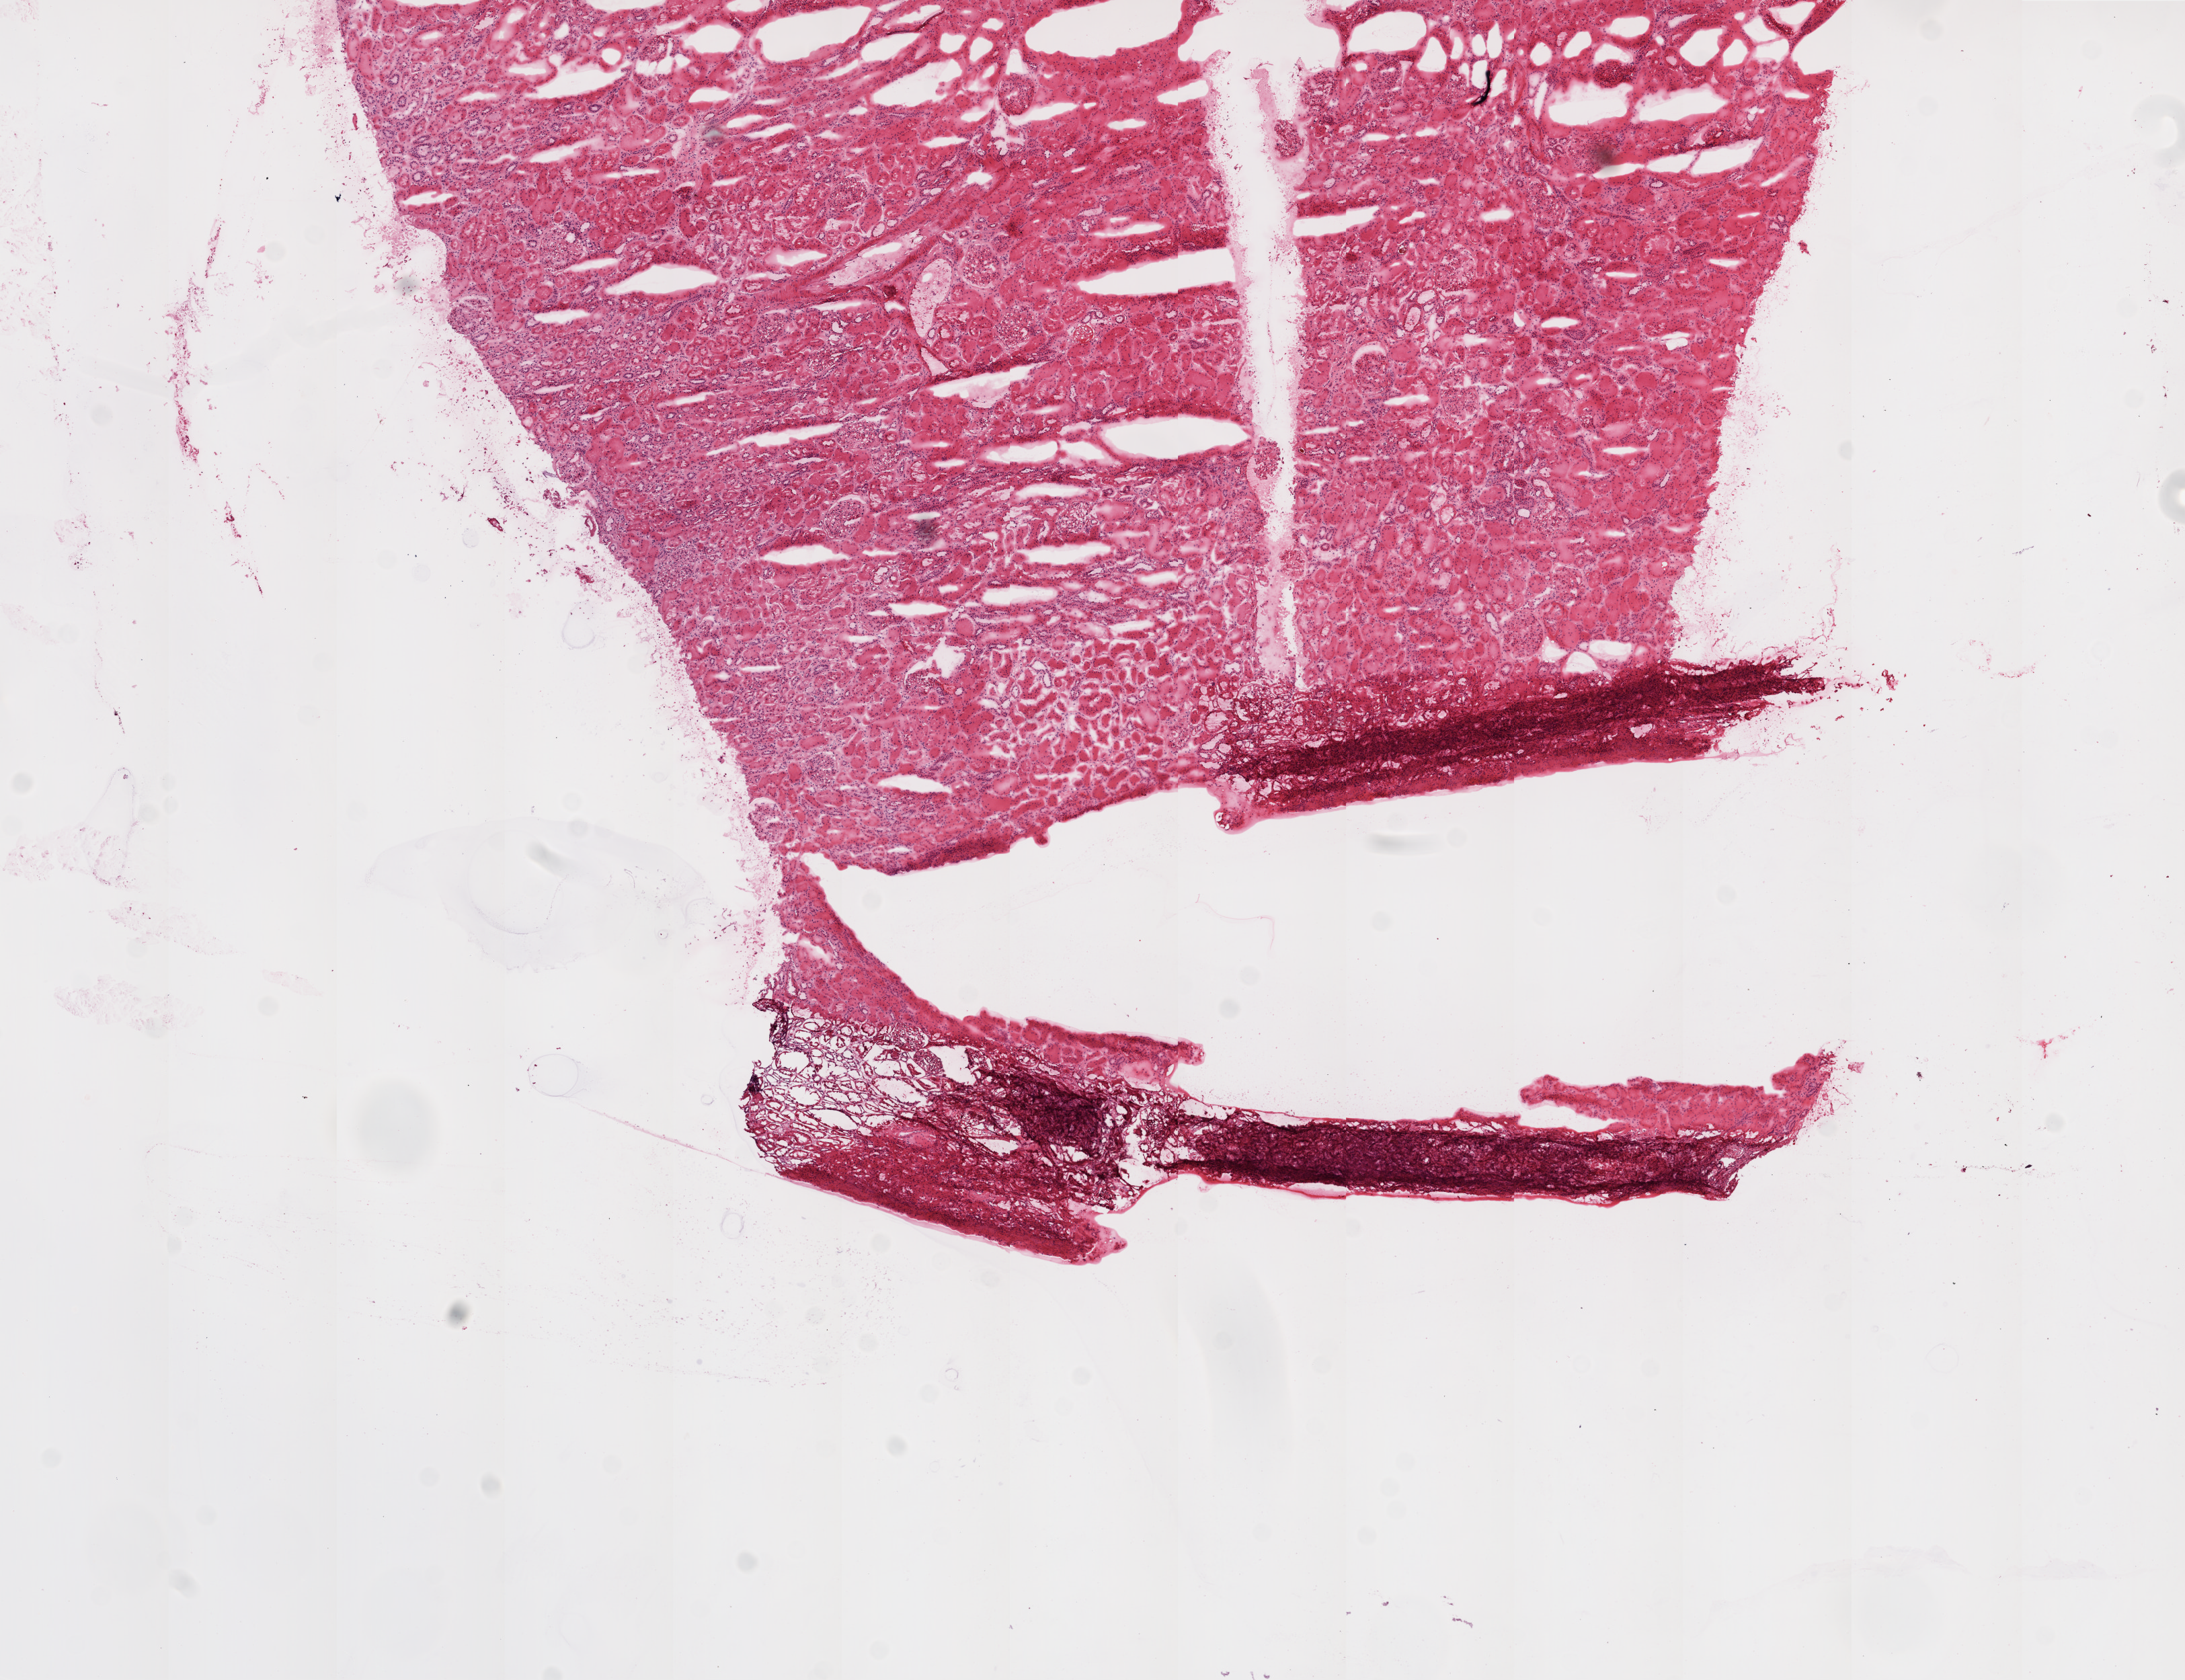
H&E whole-slide image, low-resolution overview of the scanned area, about 13.0 x 10.0 mm; frozen section from the top of the tissue portion; sample: solid tissue normal (non-tumour tissue), kidney. Patient: male, age at initial diagnosis 61 years.
This section: solid tissue normal sample (biorepository sample class). Patient diagnosis: Clear cell adenocarcinoma, NOS.